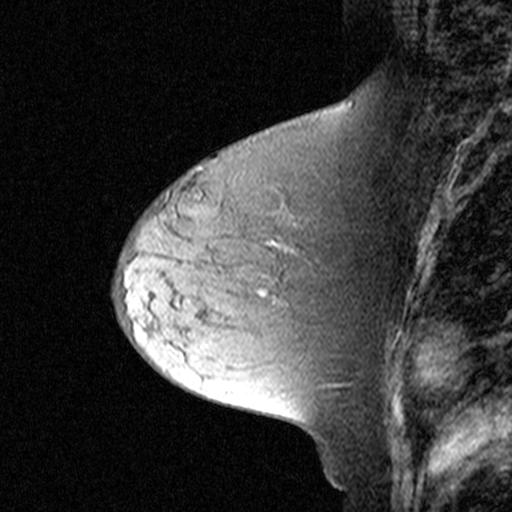
Breast MRI (dynamic contrast-enhanced), one sagittal slice; position 15 of 44 along the scan axis; dynamic contrast-enhanced study with each time point stored as its own series, time point 2 of 3 at this slice position (early post-contrast, ordered by acquisition time); 1.5 T; TE 4.5 ms, TR 11 ms; 3 mm slice thickness; 512 × 512 image matrix. Patient: female, 44 years. Case-level facts recorded for this patient, not image findings: setting: breast cancer imaged before/during neoadjuvant chemotherapy; receptor status: triple-negative.
Outlined on this slice (semi-automatically segmented with operator editing):
- analysis volume of interest (the breast-tissue region the enhancement analysis was run in; not a lesion): bounding box <174,204,303,305> (left, top, right, bottom; pixels)
- tumour enhancement mask (voxels above the 90 % enhancement threshold inside the analysis volume of interest): <260,291,266,296>